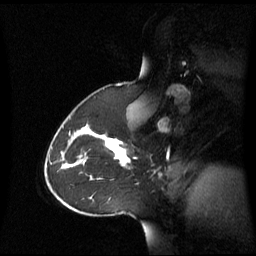
Breast MRI (dynamic contrast-enhanced), one sagittal slice; slice 42 of 60 in the series (ordered by position); dynamic contrast-enhanced series, image 2 of 3 at this slice position (ordered by acquisition); 1.5 T; TE 4.2 ms, TR 8.4 ms; 2.8 mm slice thickness; 256 × 256 image matrix. Patient: female, 43 years. Case-level facts recorded for this patient, not image findings: setting: breast cancer imaged before/during neoadjuvant chemotherapy; receptor status: triple-negative.
Structures marked on this image (semi-automatically segmented with operator editing):
- analysis volume of interest (the breast-tissue region the enhancement analysis was run in; not a lesion): box from (x=62, y=124) to (x=136, y=180) px
- tumour enhancement mask (voxels above the 70 % enhancement threshold inside the analysis volume of interest): (x=86, y=124)–(x=130, y=166)